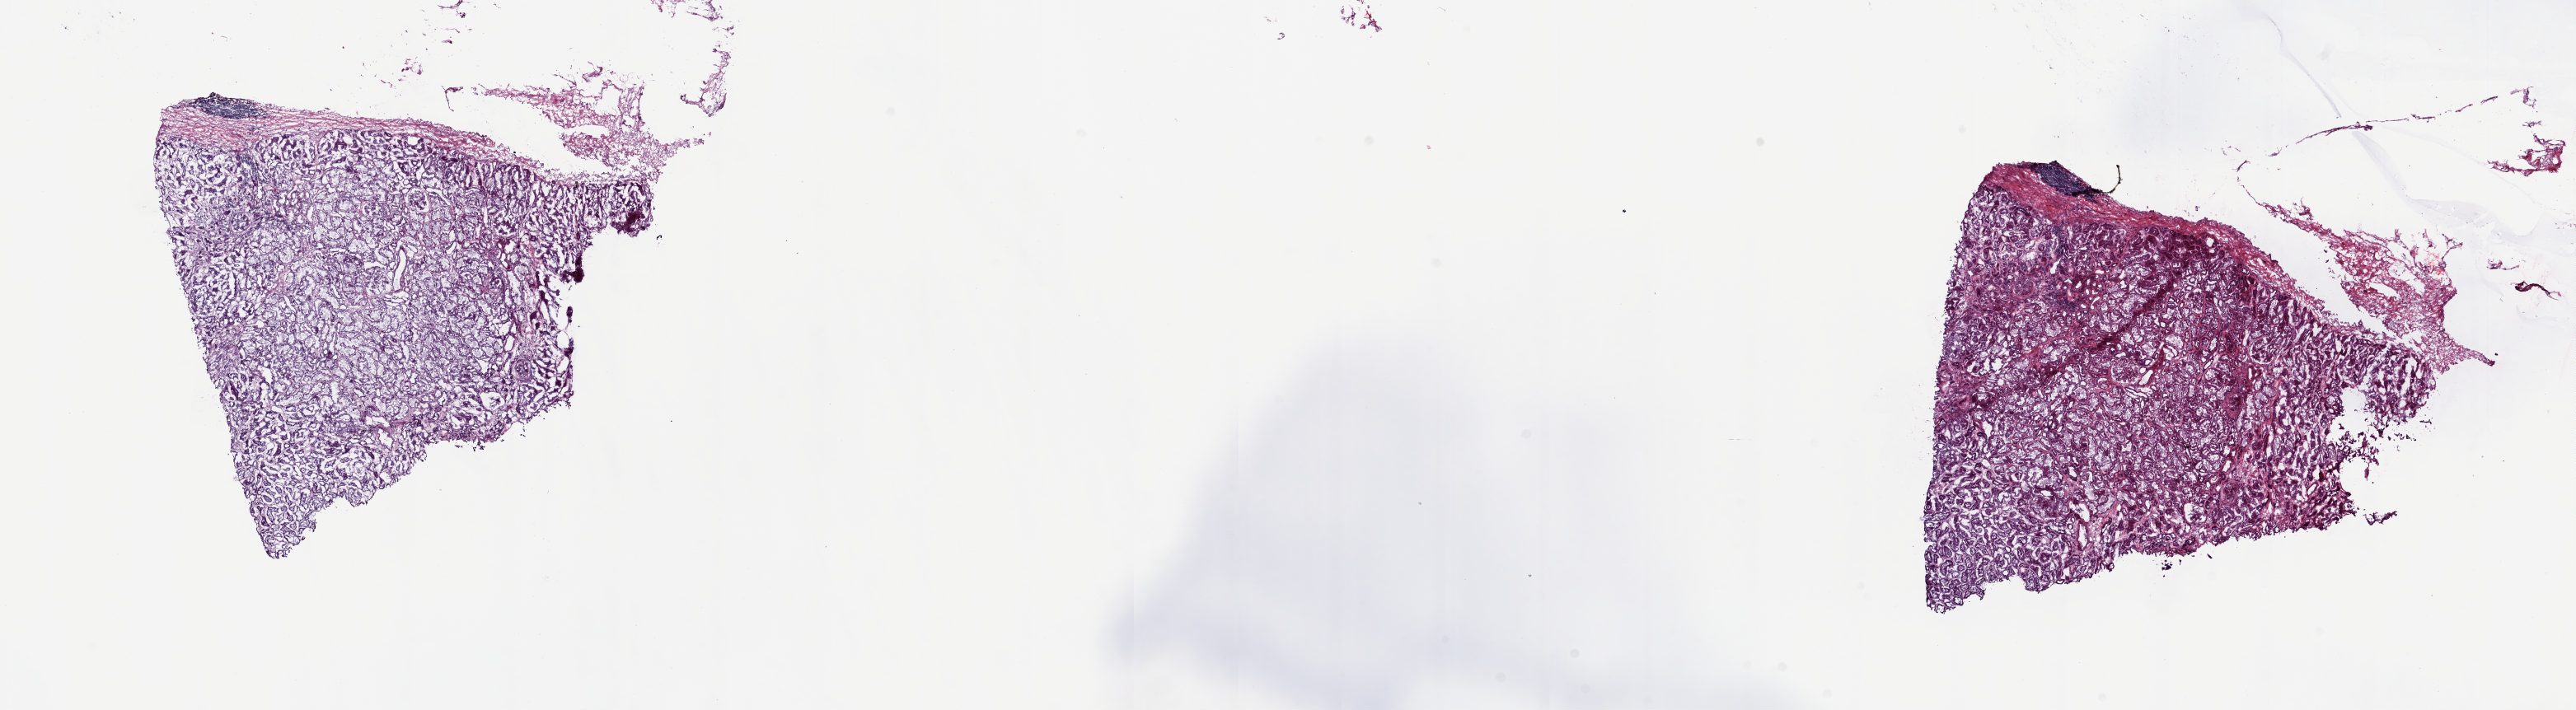
H&E-stained whole-slide image — a low-resolution overview of the entire scanned area, about 24.8 x 6.8 mm (slide scanned at 20x); frozen section from the top of the tissue portion; sample: solid tissue normal (non-tumour tissue), kidney. Patient: male, age at initial diagnosis 74 years. Pathologist review of this section (percent, as recorded): tumour cells 0%, tumour nuclei 0%, normal cells 60%, stromal cells 40%, necrosis 0%. Infiltration values recorded for this section: lymphocyte infiltration 4%, monocyte infiltration 1%, neutrophil infiltration 2%.
This section: solid tissue normal (non-tumour) sample from the same patient. Patient diagnosis: Papillary adenocarcinoma, NOS.